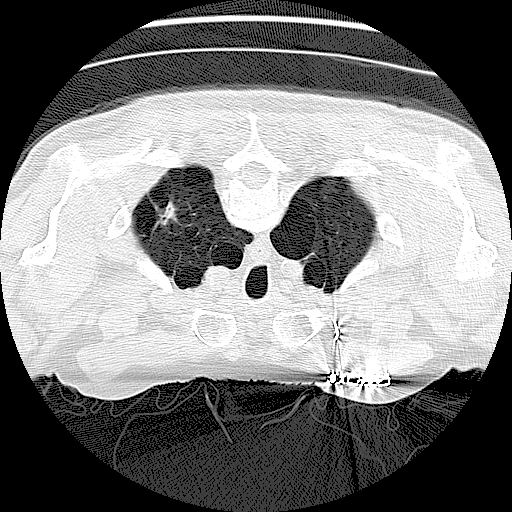
Low-dose screening chest CT, one axial slice; position 120 of 138 along the scan axis; 120 kVp; lung window (W 1500 / L -600 HU); 2.5 mm slice thickness; 512 × 512 image matrix, field of view 330 × 330 mm.
Annotated regions visible in this slice (expert manual segmentation):
- lesion 1 (tumor): bounding box (x1, y1, x2, y2) in pixels: (155, 201, 181, 227)